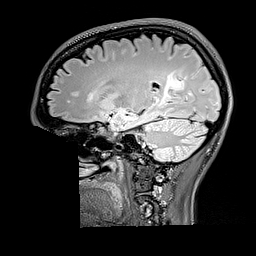
Brain MRI from a brain-tumour surgery series, one sagittal slice. Position 106 of 176 along the scan axis. T2 FLAIR. 1 mm slice thickness. 256 × 256 image matrix, field of view 256 × 256 mm. Case-level facts recorded for this patient, not image findings: histopathology: Oligodendroglioma; WHO grade: 2; IDH mutation: yes; tumour location: Right Parietal.
Structures marked on this image (manually delineated by an expert):
- tumour: bounding box (x1, y1, x2, y2) in pixels: (161, 72, 186, 105)